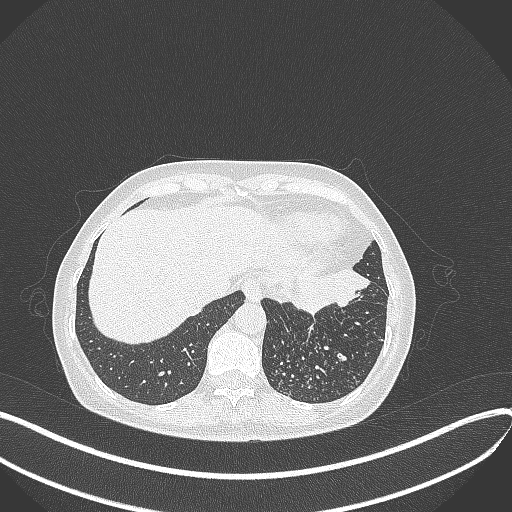
Chest CT, one axial slice; slice 86 of 429 in the series (ordered by position); reconstruction kernel B70f; 100 kVp; lung window (W 1500 / L -600 HU); 512 × 512 image matrix, field of view 400 × 400 mm. Patient: female, 63 years. Case-level facts recorded for this patient, not image findings: clinical TNM (as recorded): T1b N0 M0; histopathological grade: G2-3.
Outlined on this slice (bounding box drawn by a radiologist):
- lung tumour (recorded histology: adenocarcinoma): bounding box [x1, y1, x2, y2] px = [288, 269, 371, 311]